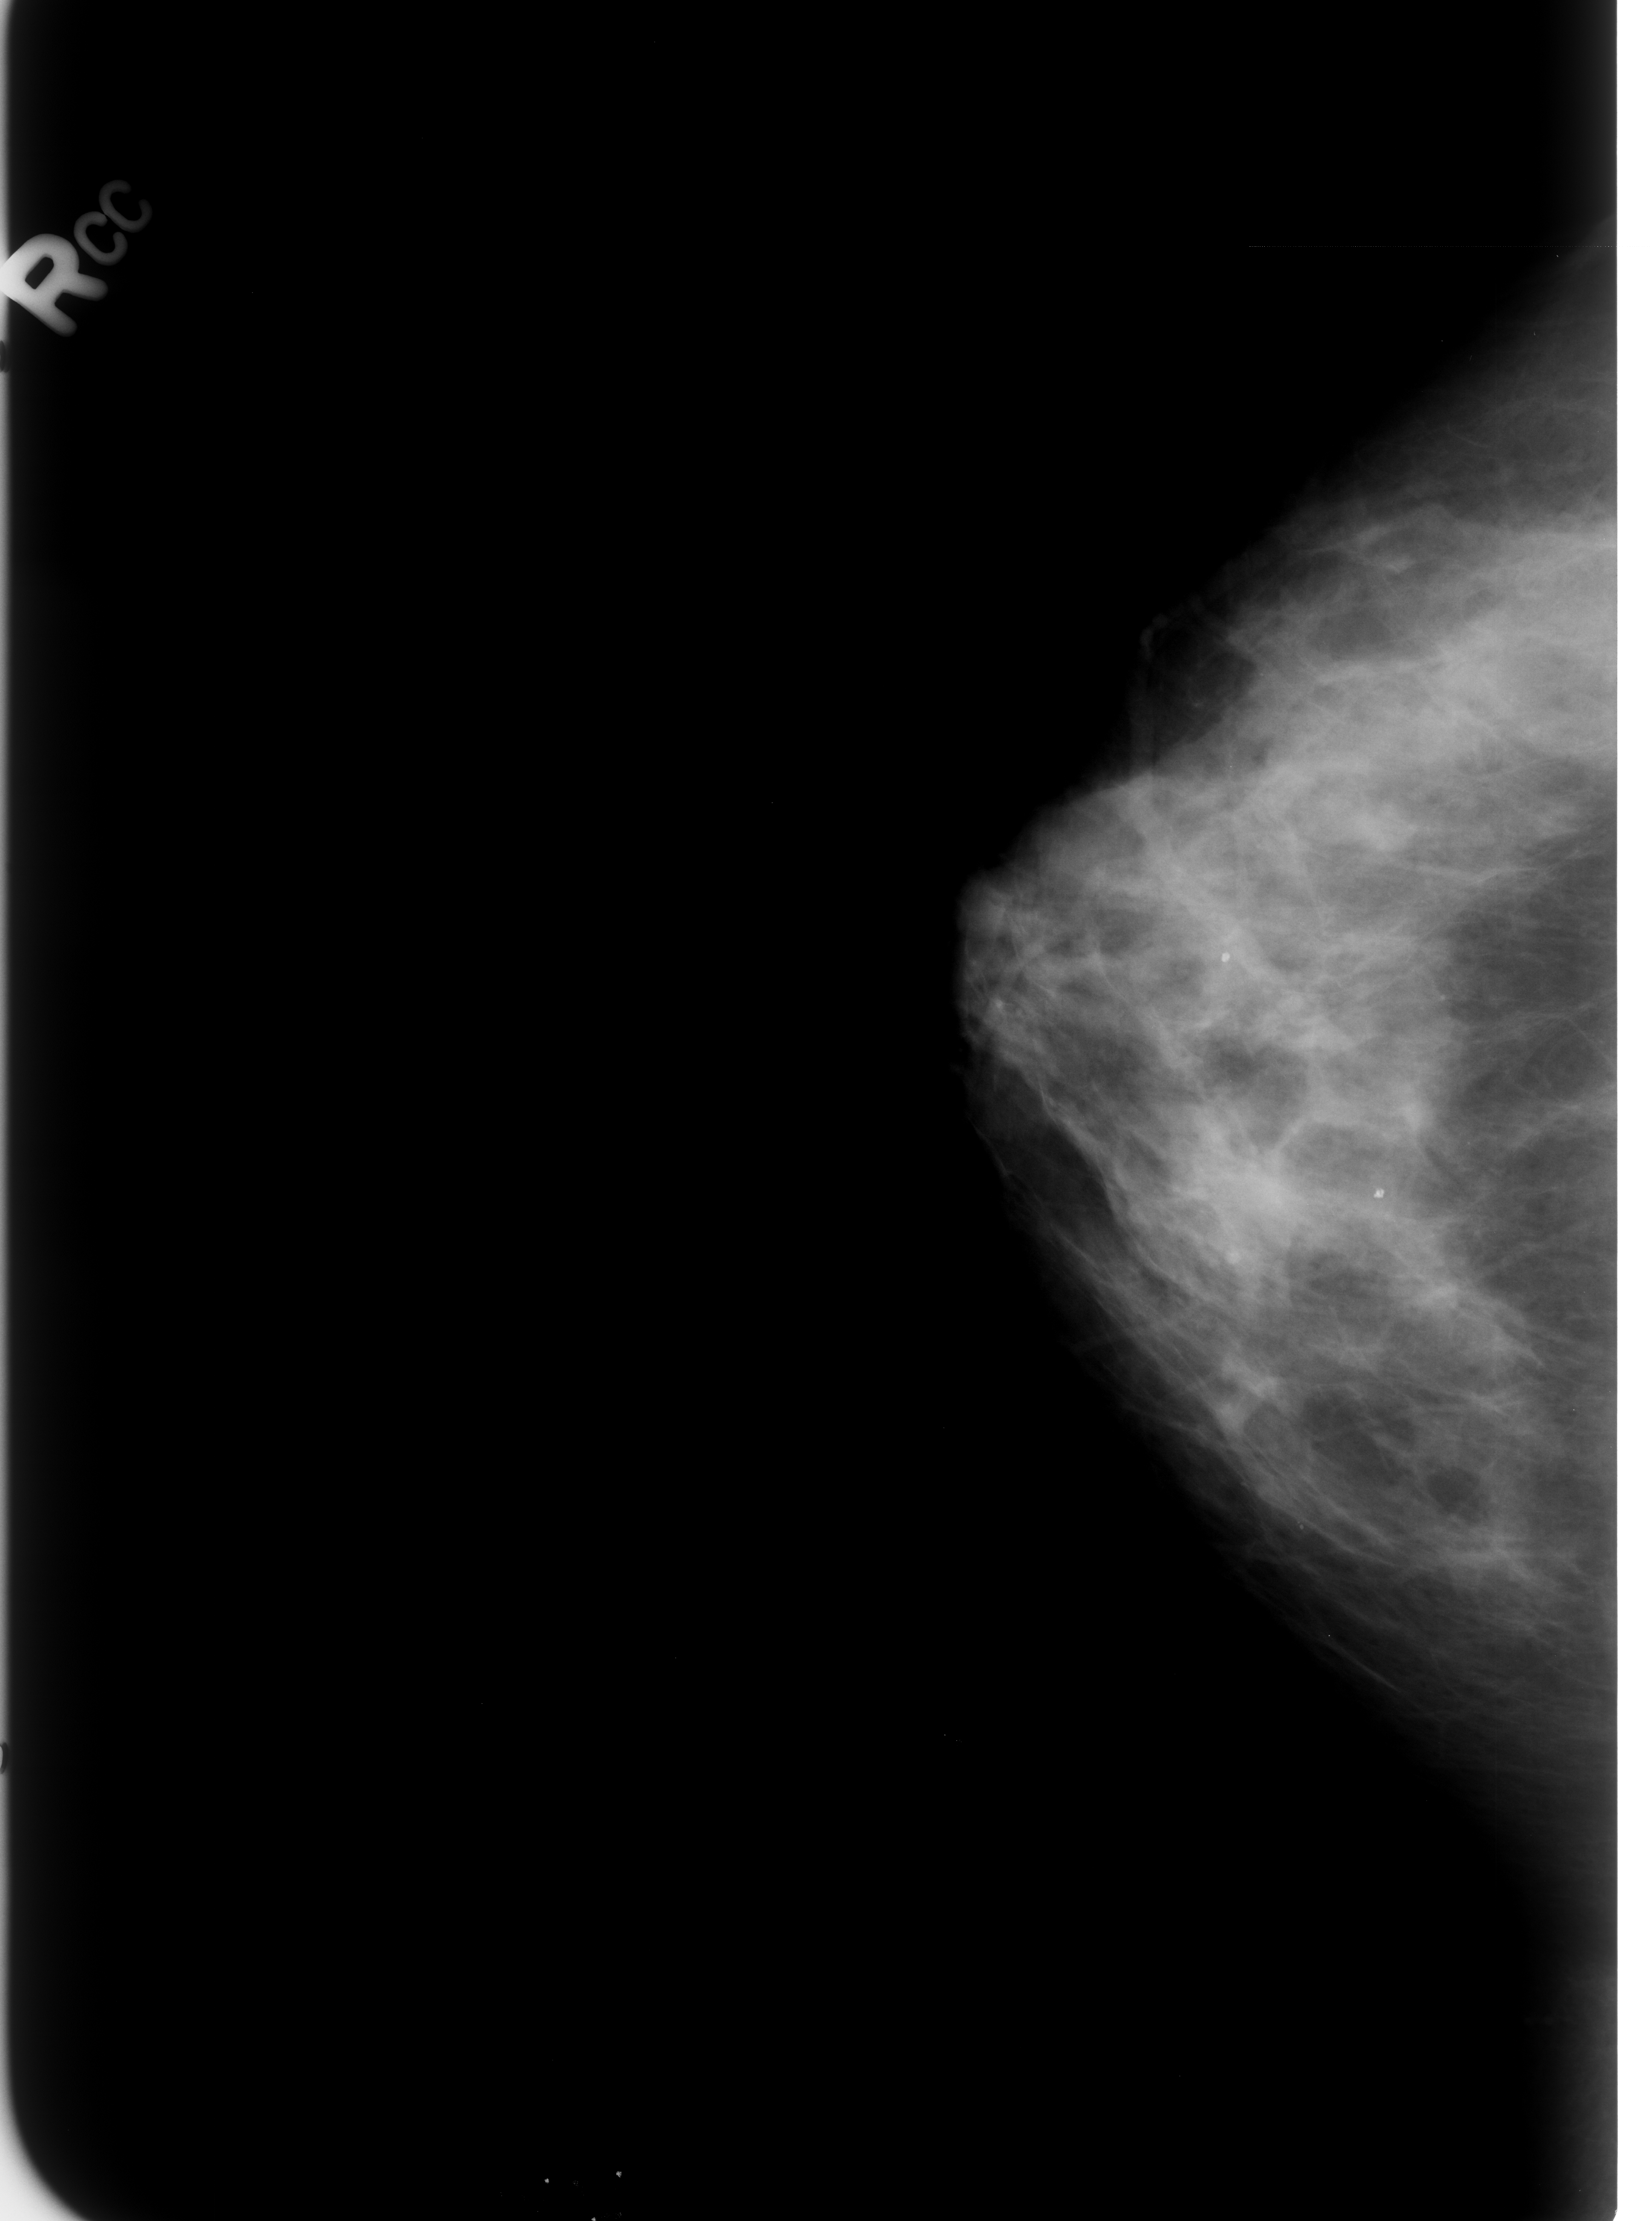
Scanned film-screen mammogram; right breast; craniocaudal (CC) view; BI-RADS breast density category 3 (scale 1–4).
Abnormality record for this image: Finding 1 of 2: calcifications, morphology lucent center; BI-RADS assessment category 2; subtlety rating 5 on a 1 (subtle) to 5 (obvious) scale; benign without callback (not worked up further). Finding 2 of 2: calcifications, morphology lucent center; BI-RADS assessment category 2; benign without callback (not worked up further).